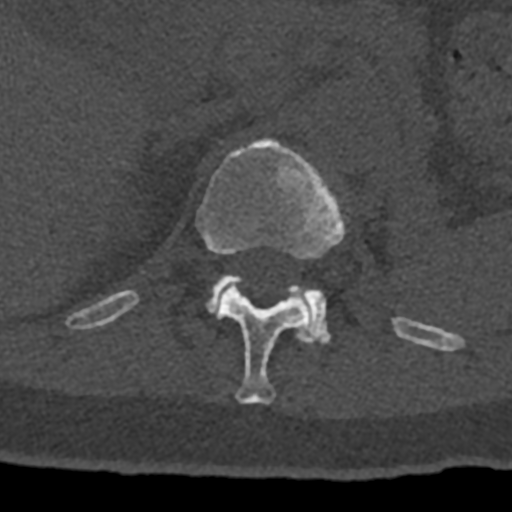
CT including the spine, one axial slice; position 477 of 797 along the scan axis; reconstruction kernel Br40s/3; 120 kVp; bone window (W 1800 / L 400 HU); 0.5 mm slice thickness; 512 × 512 image matrix, field of view 160 × 160 mm. Patient: male, 74 years. From the clinical record (not read from this slice): primary cancer: renal; vertebrae with lytic lesions (as recorded): T10, L1, L2, L3, L4, L5.
Structures marked on this image (semi-automatic segmentation, software-assisted and operator-edited):
- L1 vertebra: bounding box (x1, y1, x2, y2) in pixels: (207, 275, 330, 343)
- T12 vertebra: (70, 139, 432, 404)